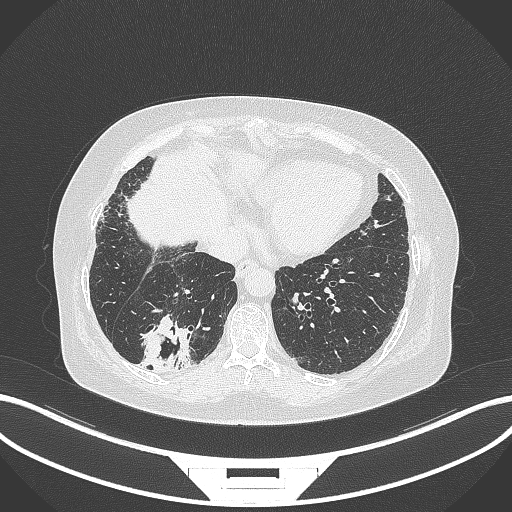
Chest CT, one axial slice; position 57 of 296 along the scan axis; 120 kVp; lung window (W 1500 / L -600 HU); 512 × 512 image matrix, field of view 400 × 400 mm. Patient: female, 65 years. Case-level facts recorded for this patient, not image findings: clinical TNM (as recorded): T2b N1 M0; histopathological grade: G1.
Annotated regions visible in this slice (rectangle marked by the reading radiologist):
- lung tumour (recorded histology: adenocarcinoma): bounding box <133,315,196,374> (left, top, right, bottom; pixels)